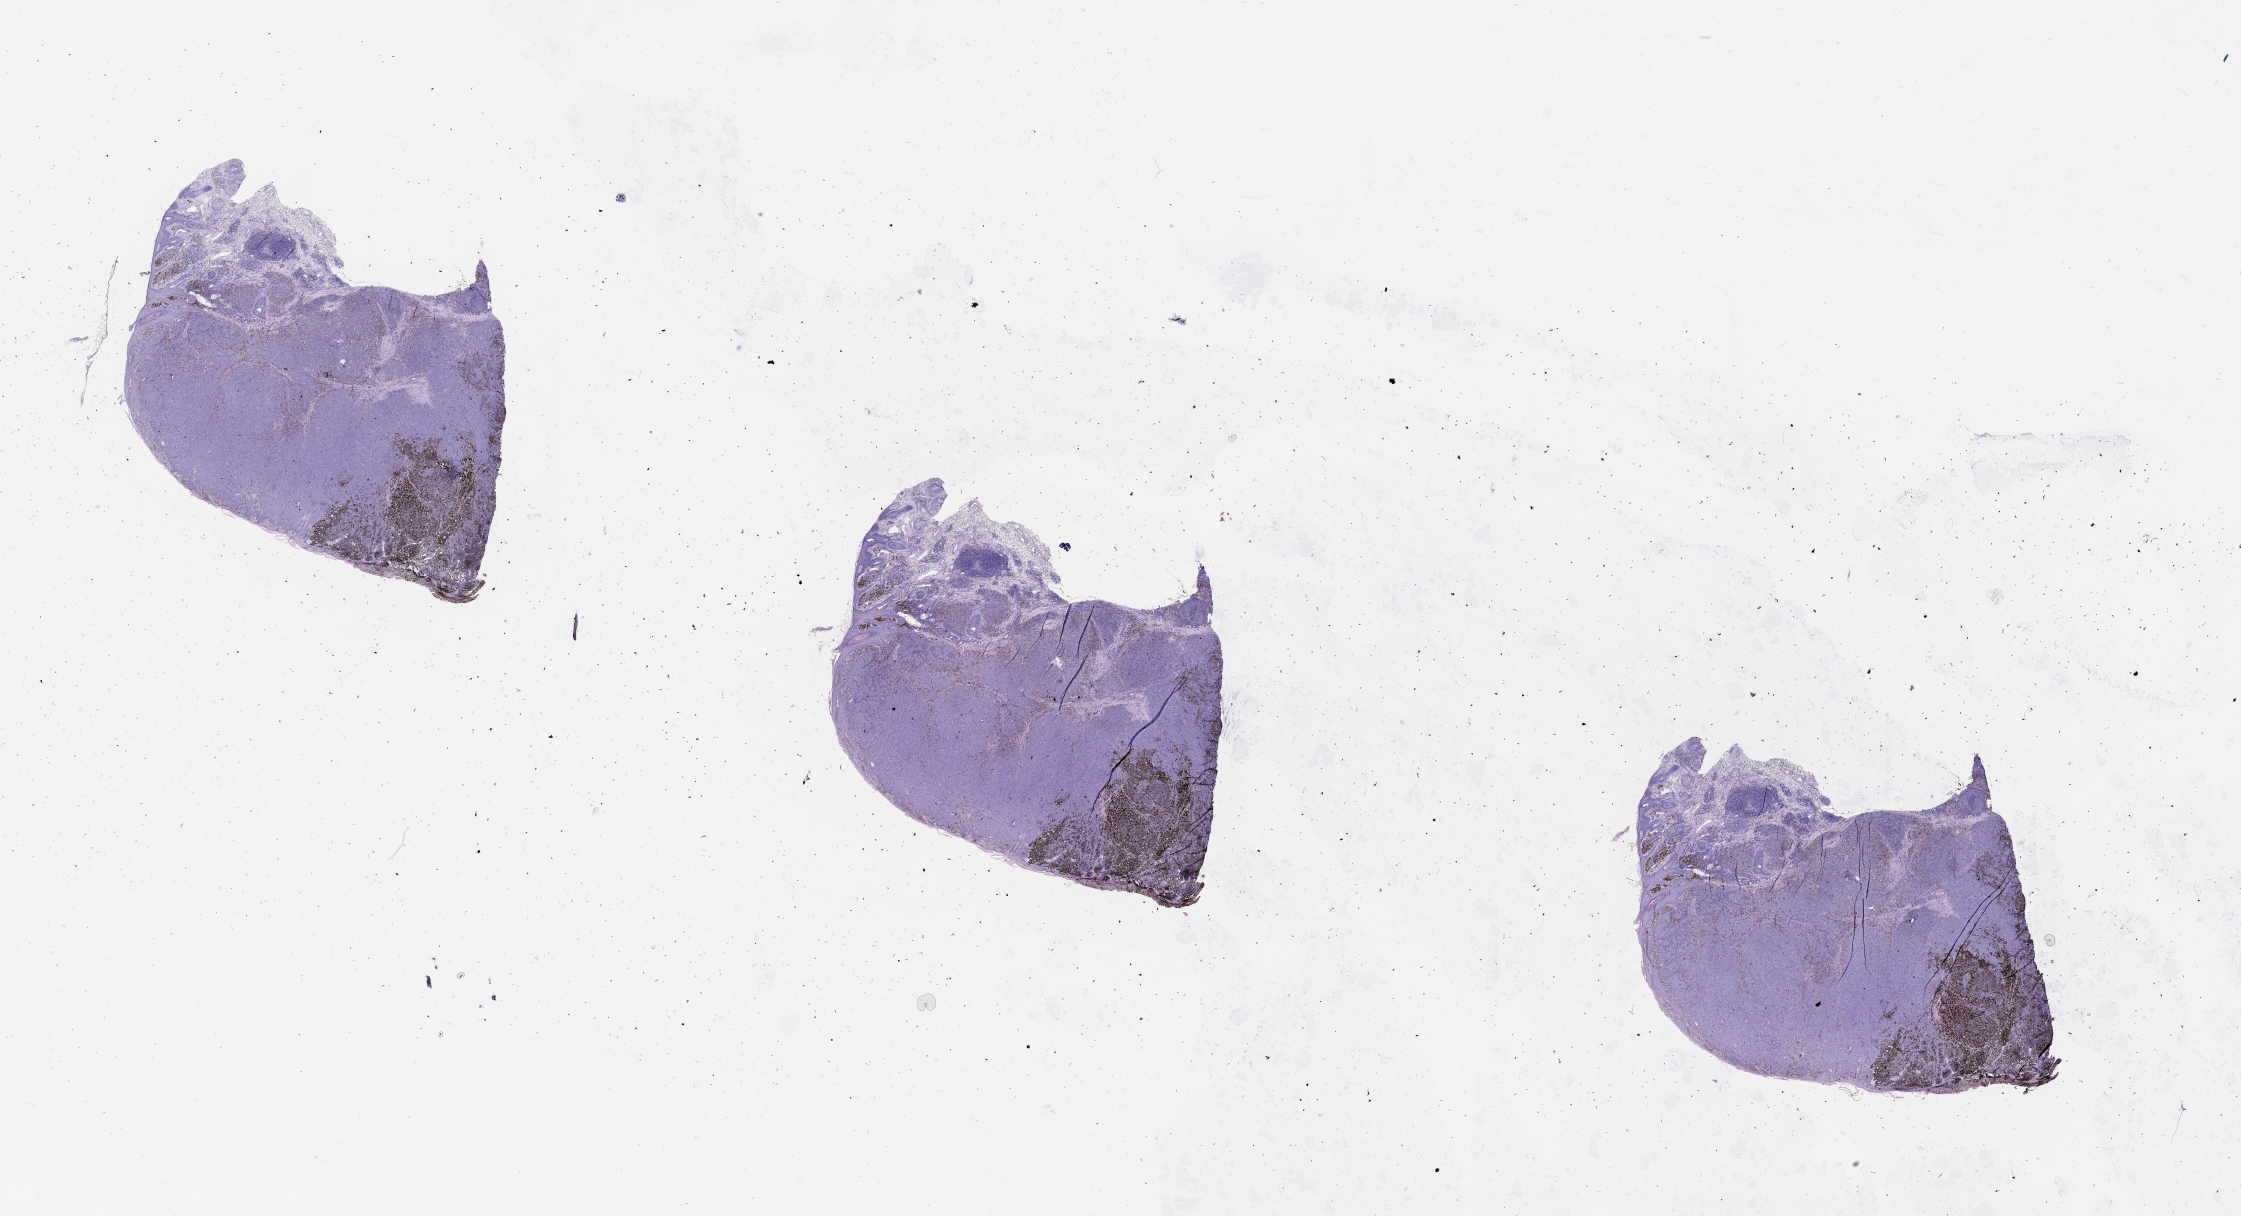
Whole-slide histology image, Hematoxylin and eosin (H&E) stained — shown as a low-resolution overview of the whole scanned area (about 36.1 x 19.6 mm); tumour tissue sample, sampled site: head & neck. Patient: male, age 83 years. Pathologist review of this section (percent, as recorded): tumour nuclei 80%, necrosis 0%.
Histologic diagnosis: Malignant melanoma, NOS. AJCC pathologic stage: IIC. Primary tumour site (as recorded): head & neck.